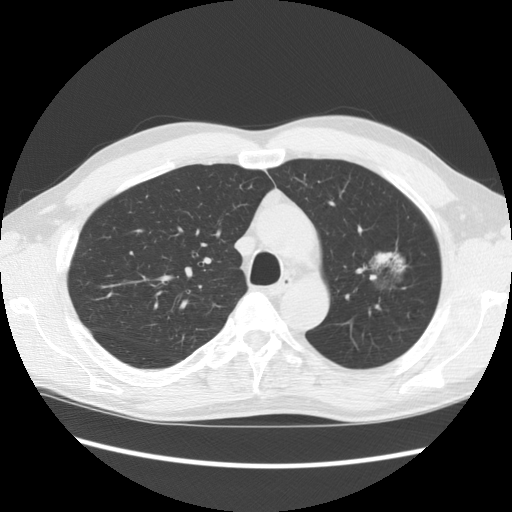
Chest CT (low-dose screening protocol), one axial image, second screening round (one year after baseline), lung window (W 1500 / L -600 HU). Male participant, aged 61 years at enrolment. Former smoker at enrolment.
Expert reader's lesion annotation, bounding box [x1, y1, x2, y2] px = [348, 225, 423, 298]. The exam's reader record, not a measurement of the box and not confirmed to be the same lesion: non-calcified nodule or mass ≥4 mm, left upper lobe, 34 × 32 mm, poorly defined margins, mixed attenuation, pre-existing on the prior screen: yes; interval growth: no. Official screen result: positive, no significant change: stable abnormalities potentially related to lung cancer, unchanged since the prior screening exam.